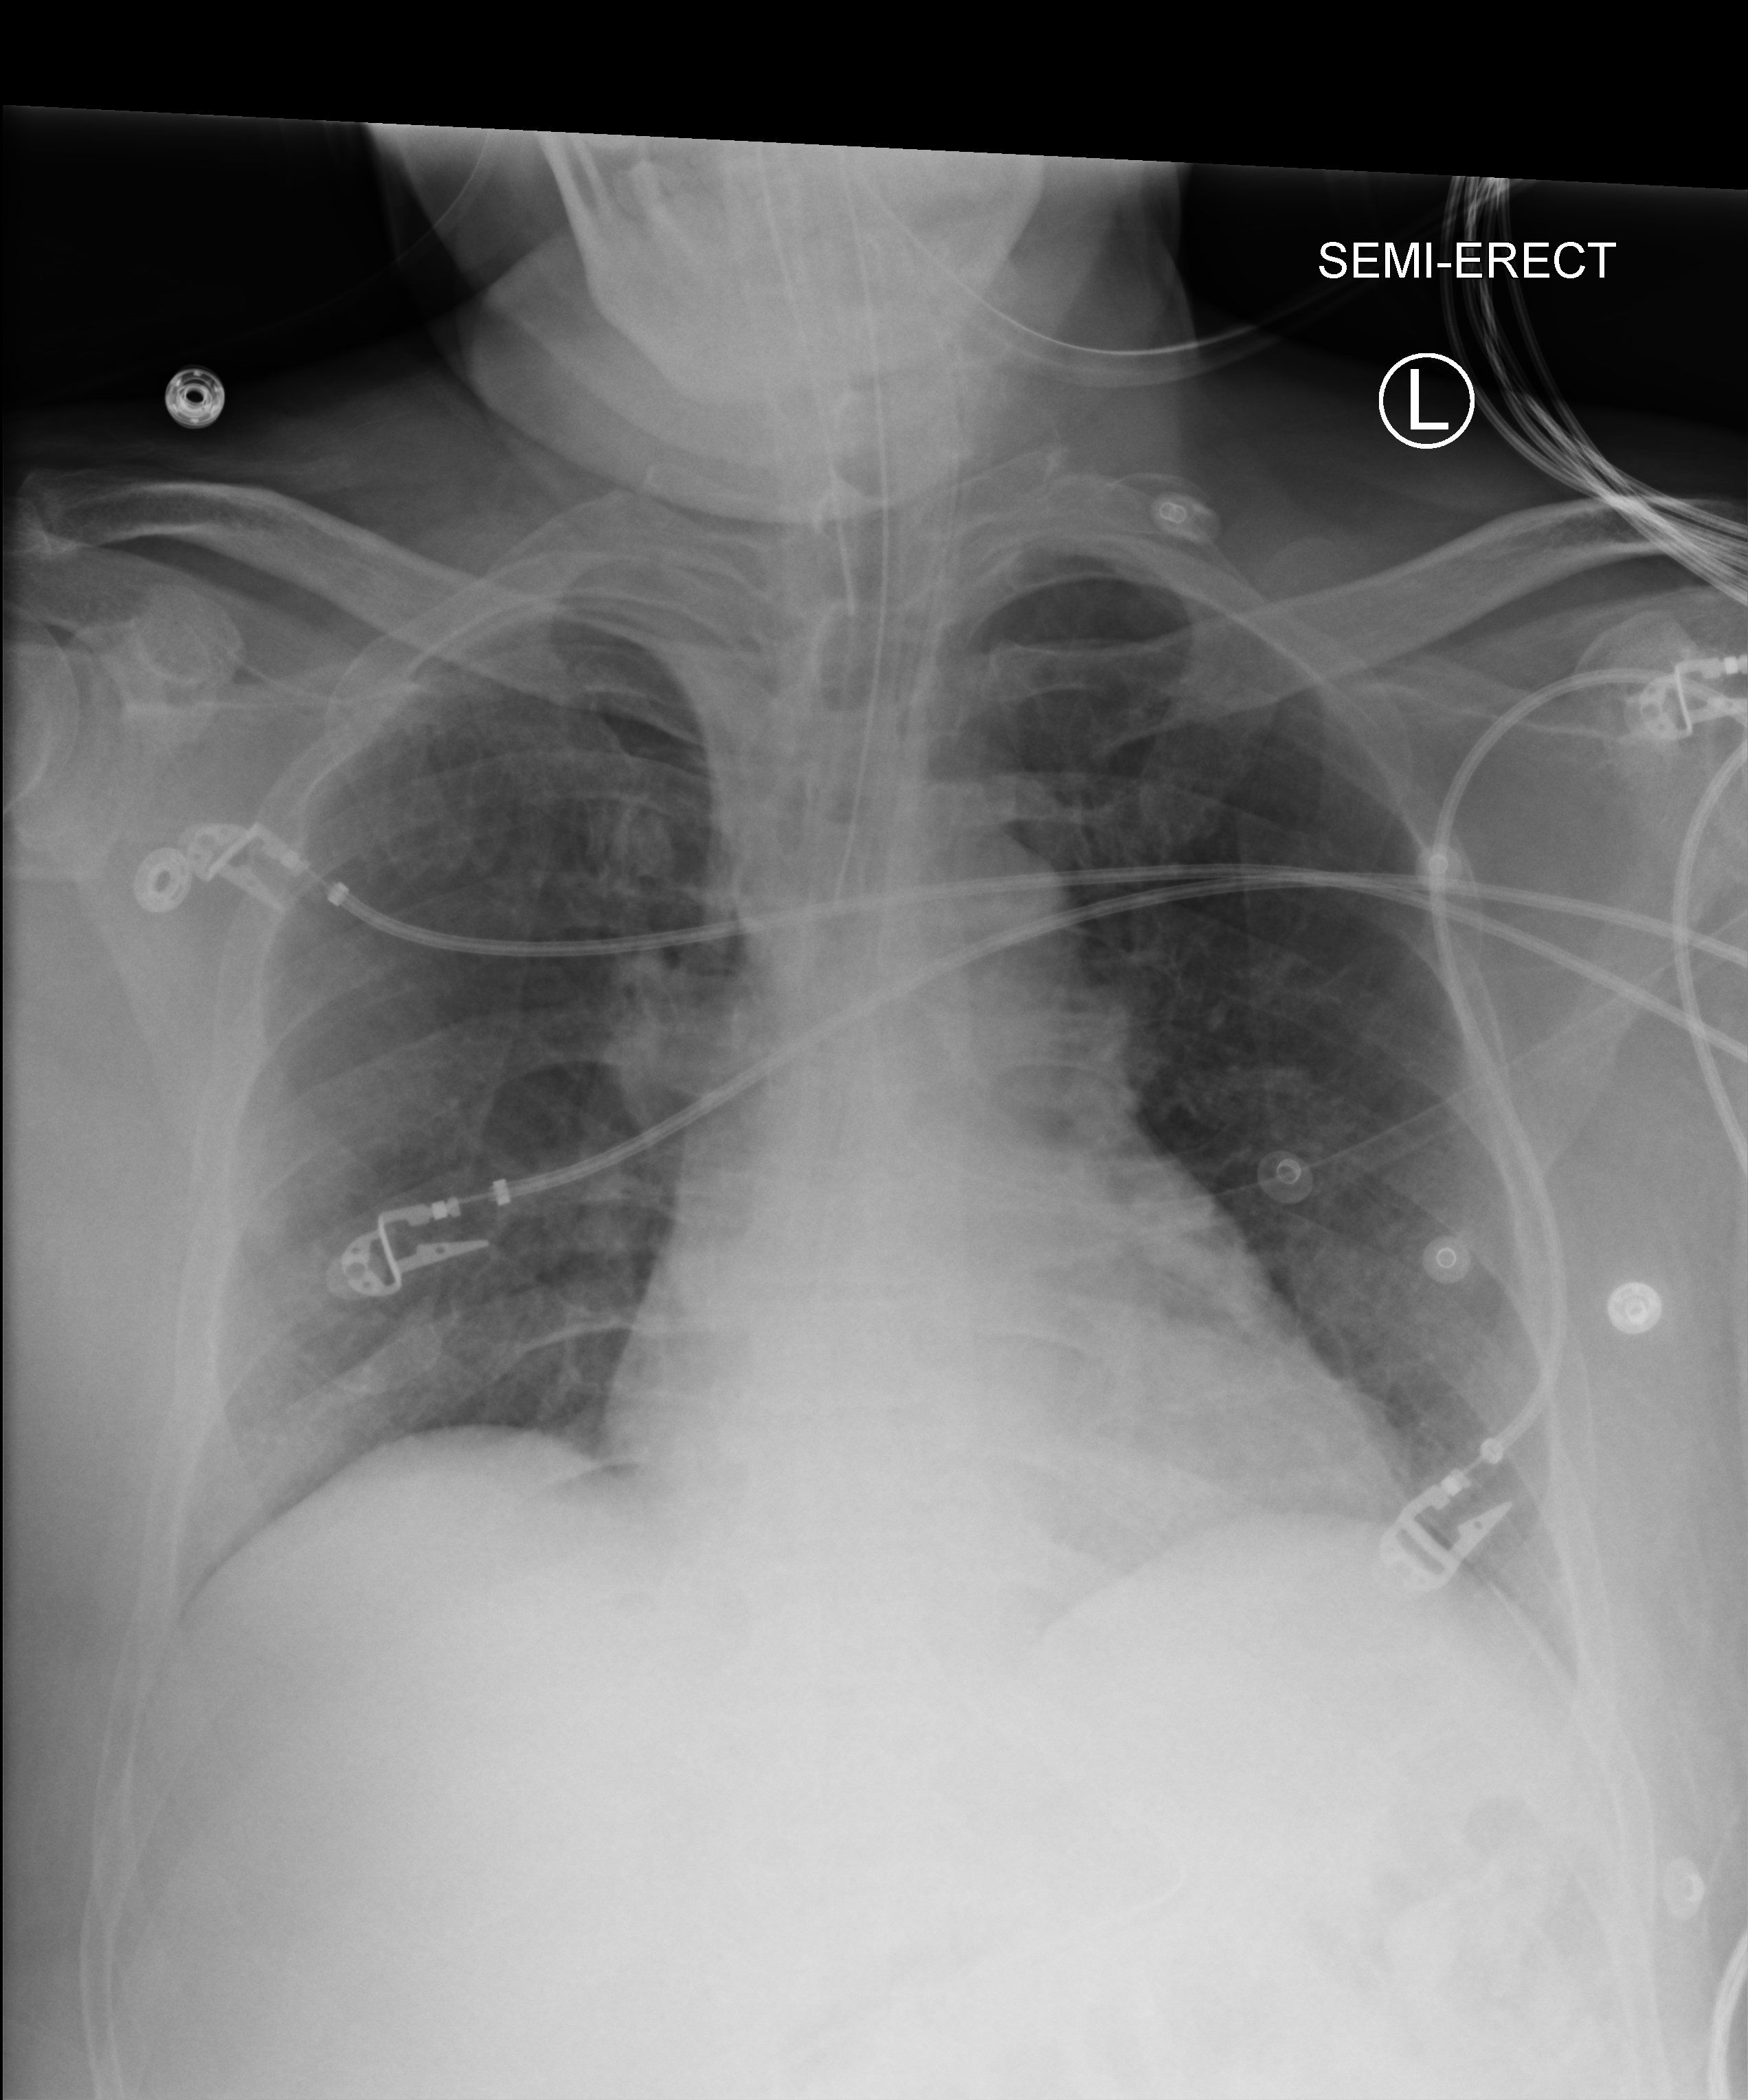
Bedside chest radiograph (computed radiography). Adult patient hospitalised with COVID-19, age 18–59 years.
Hospital-stay facts (about this admission, not read from this image; timing relative to this image not recorded): length of hospital stay: 37 days; mechanically ventilated during this hospital stay: yes; admitted to intensive care during this hospital stay: yes.